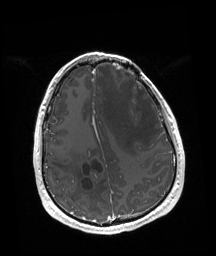
Brain MRI from a brain-tumour surgery series, one axial slice. Position 55 of 192 along the scan axis. T1-weighted post-contrast. 1 mm slice thickness. 216 × 256 image matrix, field of view 219 × 260 mm. Case-level facts recorded for this patient, not image findings: tumour location: Left Frontal.
Outlined on this slice (expert manual segmentation):
- tumour: box from (x=126, y=69) to (x=134, y=75) px